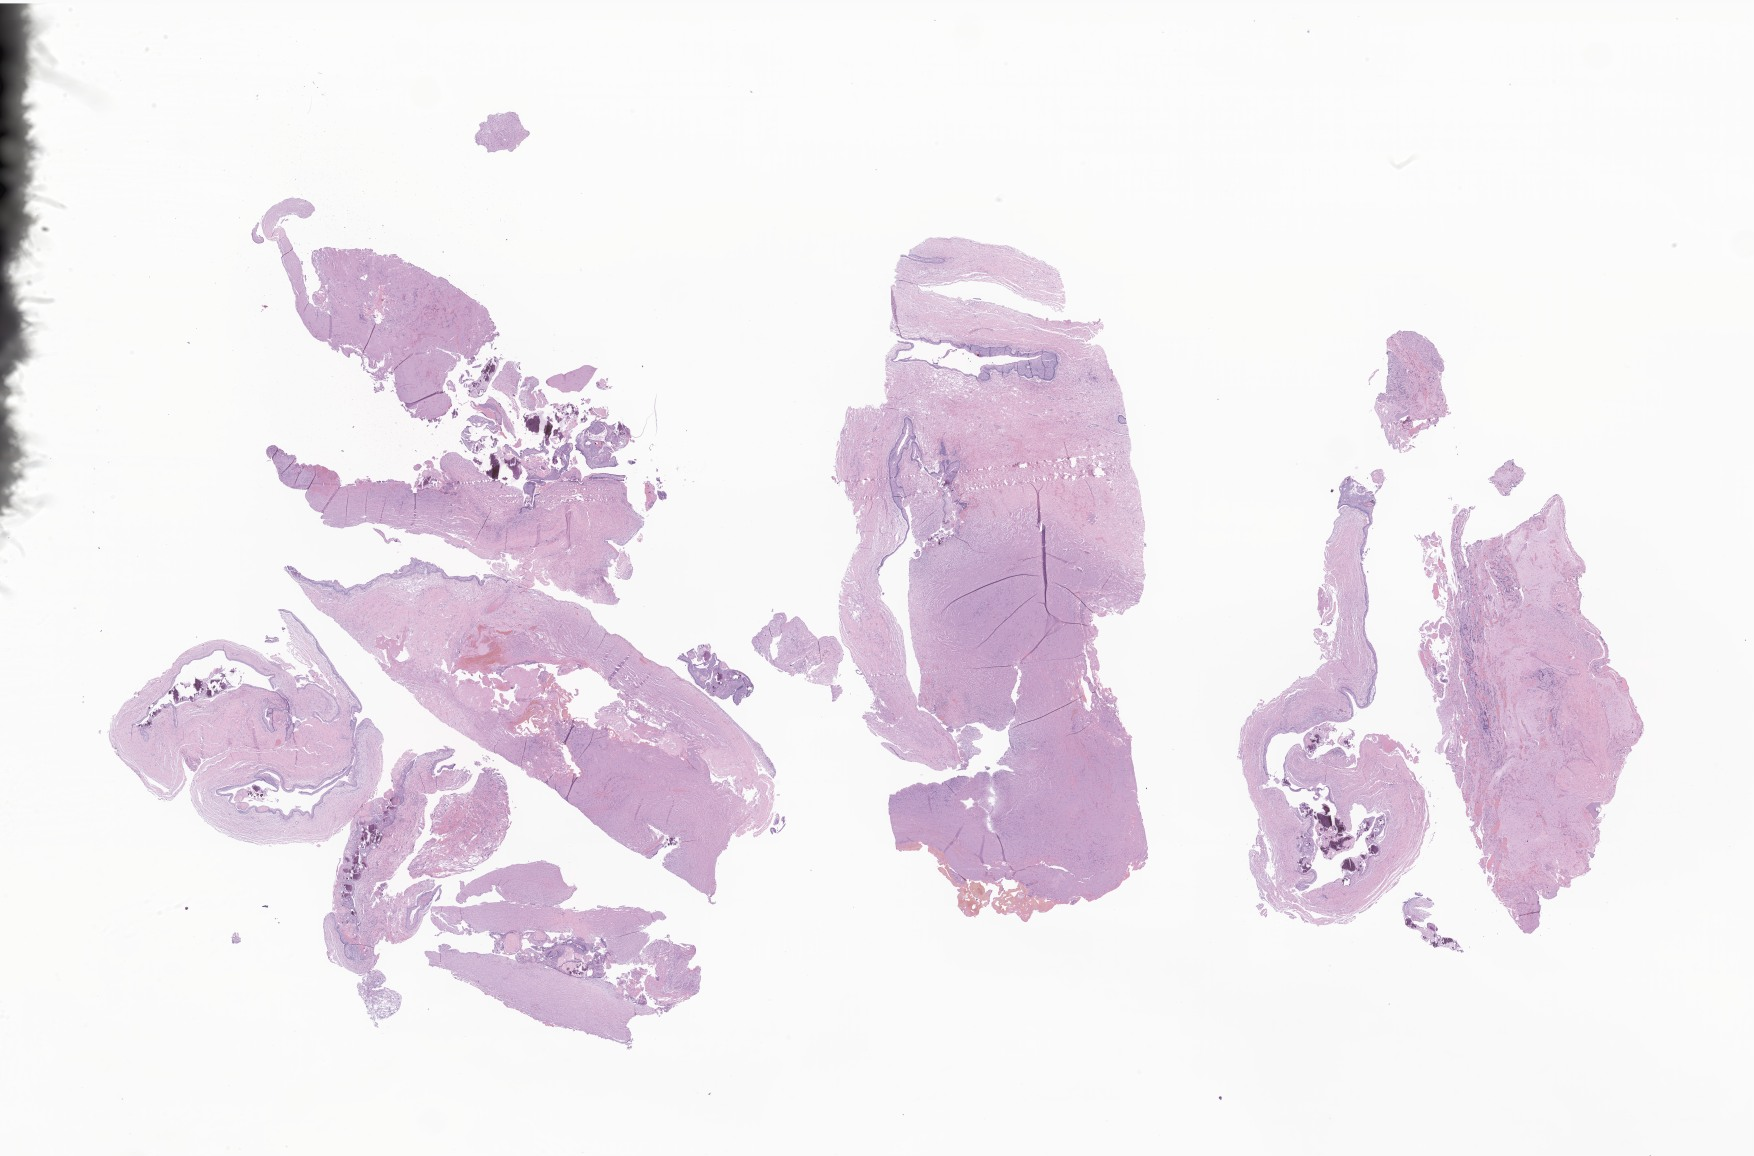
Whole-slide image, hematoxylin and eosin (H&E) stain of tumor tissue from the pituitary gland — a low-resolution overview of the entire scanned area, about 29.6 x 19.5 mm, FFPE section. Patient female; age 156 months (13 years).
Recorded diagnosis: Craniopharyngioma, adamantinomatous.